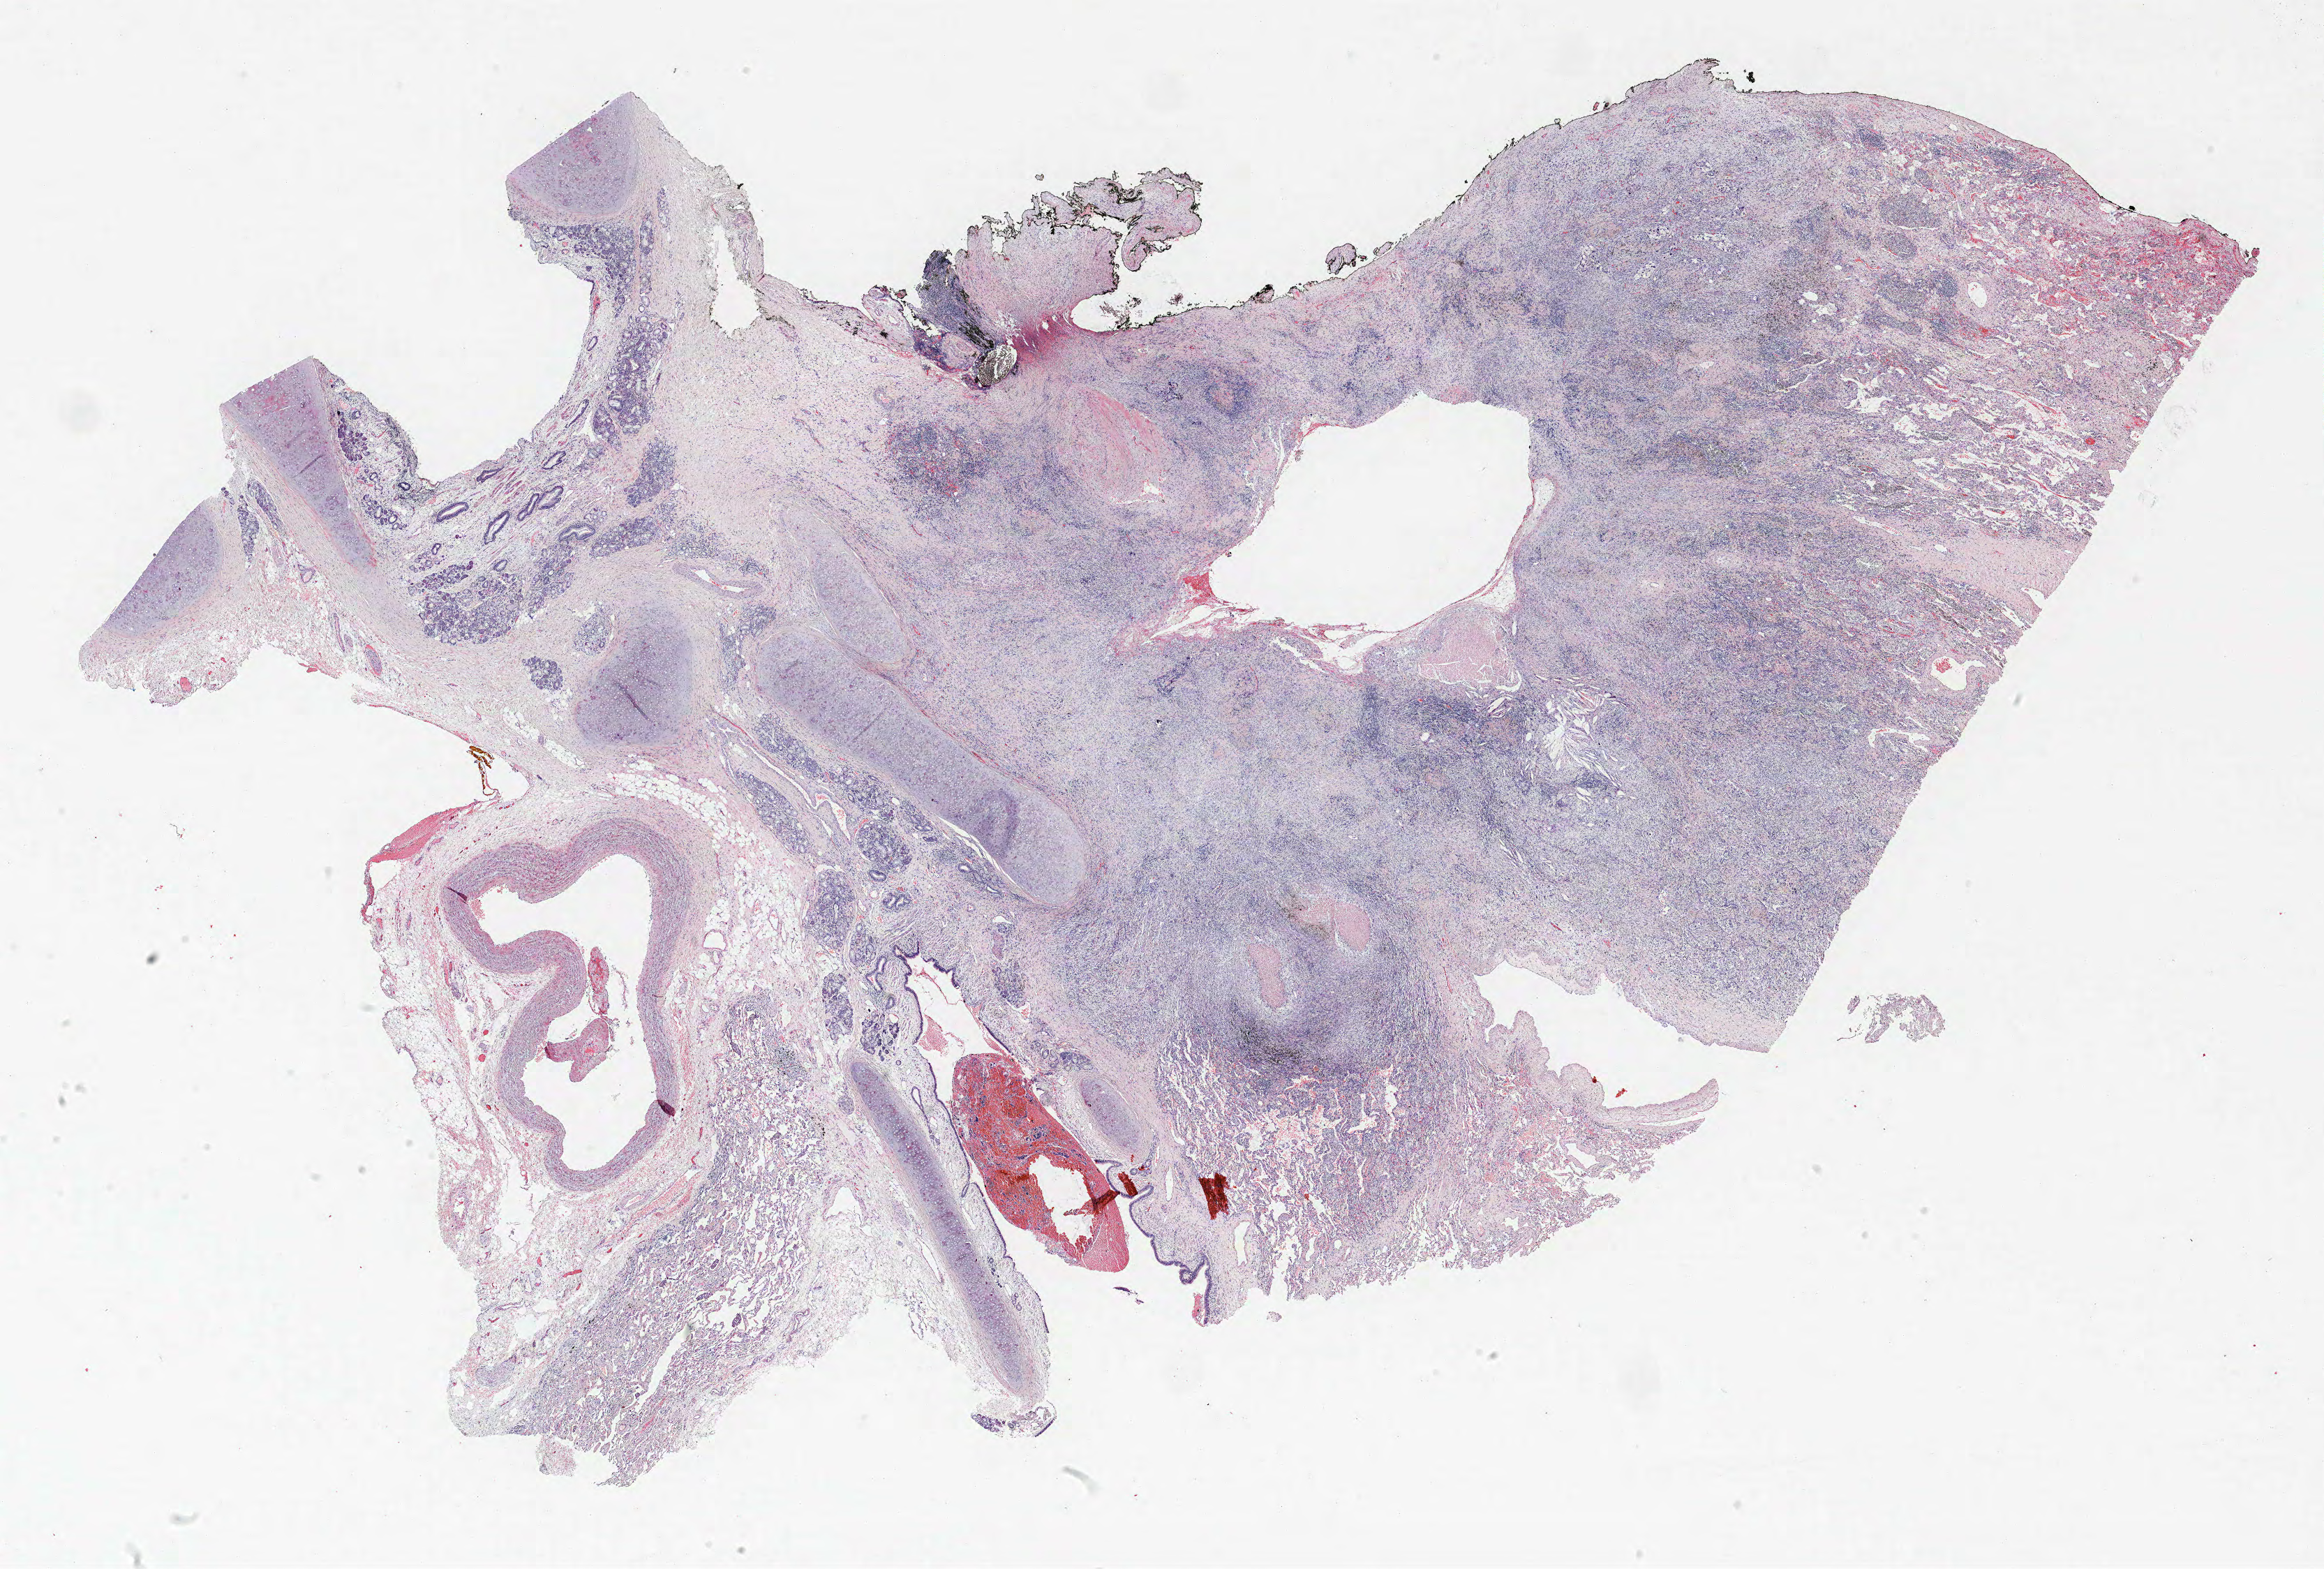
Whole-slide histology image, H&E — shown as a low-resolution overview of the whole scanned area (about 26.6 x 18.0 mm). Formalin-fixed paraffin-embedded (FFPE) section. Lung. Female patient, aged 61 at enrolment. Former smoker at enrolment. Grade: poorly differentiated (G3).
Stage (AJCC 6th edition): IB. Primary tumour location (clinical record): left upper lobe. Participant's lung-cancer diagnosis: Squamous cell carcinoma, NOS (ICD-O-3 8070/3). Tumour size (pathology): 30 mm.